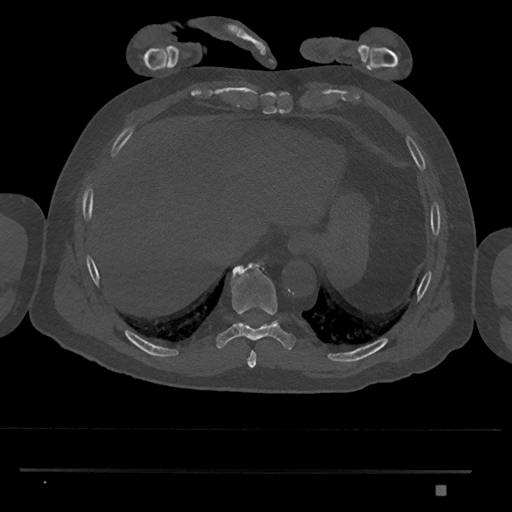
CT including the spine, one axial slice; position 1054 of 1134 along the scan axis; reconstruction kernel Br40s/3; bone window (W 1800 / L 400 HU); 0.5 mm slice thickness; 512 × 512 image matrix. Male patient, age 65 years. From the clinical record (not read from this slice): primary cancer: prostate.
Structures marked on this image (semi-automatically segmented with operator editing):
- T10 vertebra: bounding box [x1, y1, x2, y2] px = [273, 320, 279, 323]
- T8 vertebra: [247, 351, 257, 367]
- T9 vertebra: [216, 263, 296, 350]